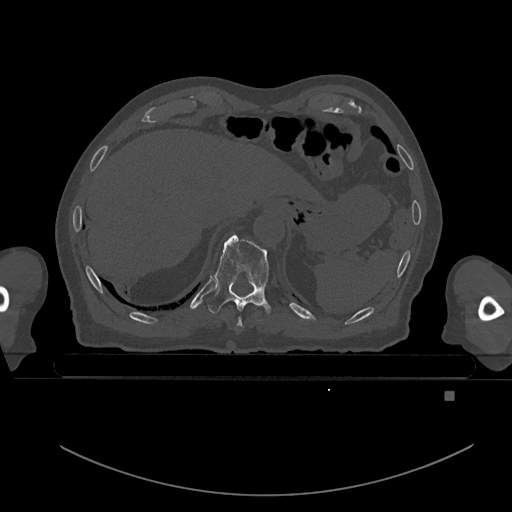
CT including the spine, one axial slice; slice 92 of 969 in the series (ordered by position); bone window (W 1800 / L 400 HU); 512 × 512 image matrix. Male patient, age 82 years. Case-level facts recorded for this patient, not image findings: primary cancer: prostate; vertebrae with lytic lesions (as recorded): T11, T9, T8, T2.
Outlined on this slice (semi-automatic segmentation, software-assisted and operator-edited):
- T10 vertebra: box from (x=207, y=234) to (x=272, y=315) px
- T9 vertebra: (x=237, y=317)–(x=243, y=329)